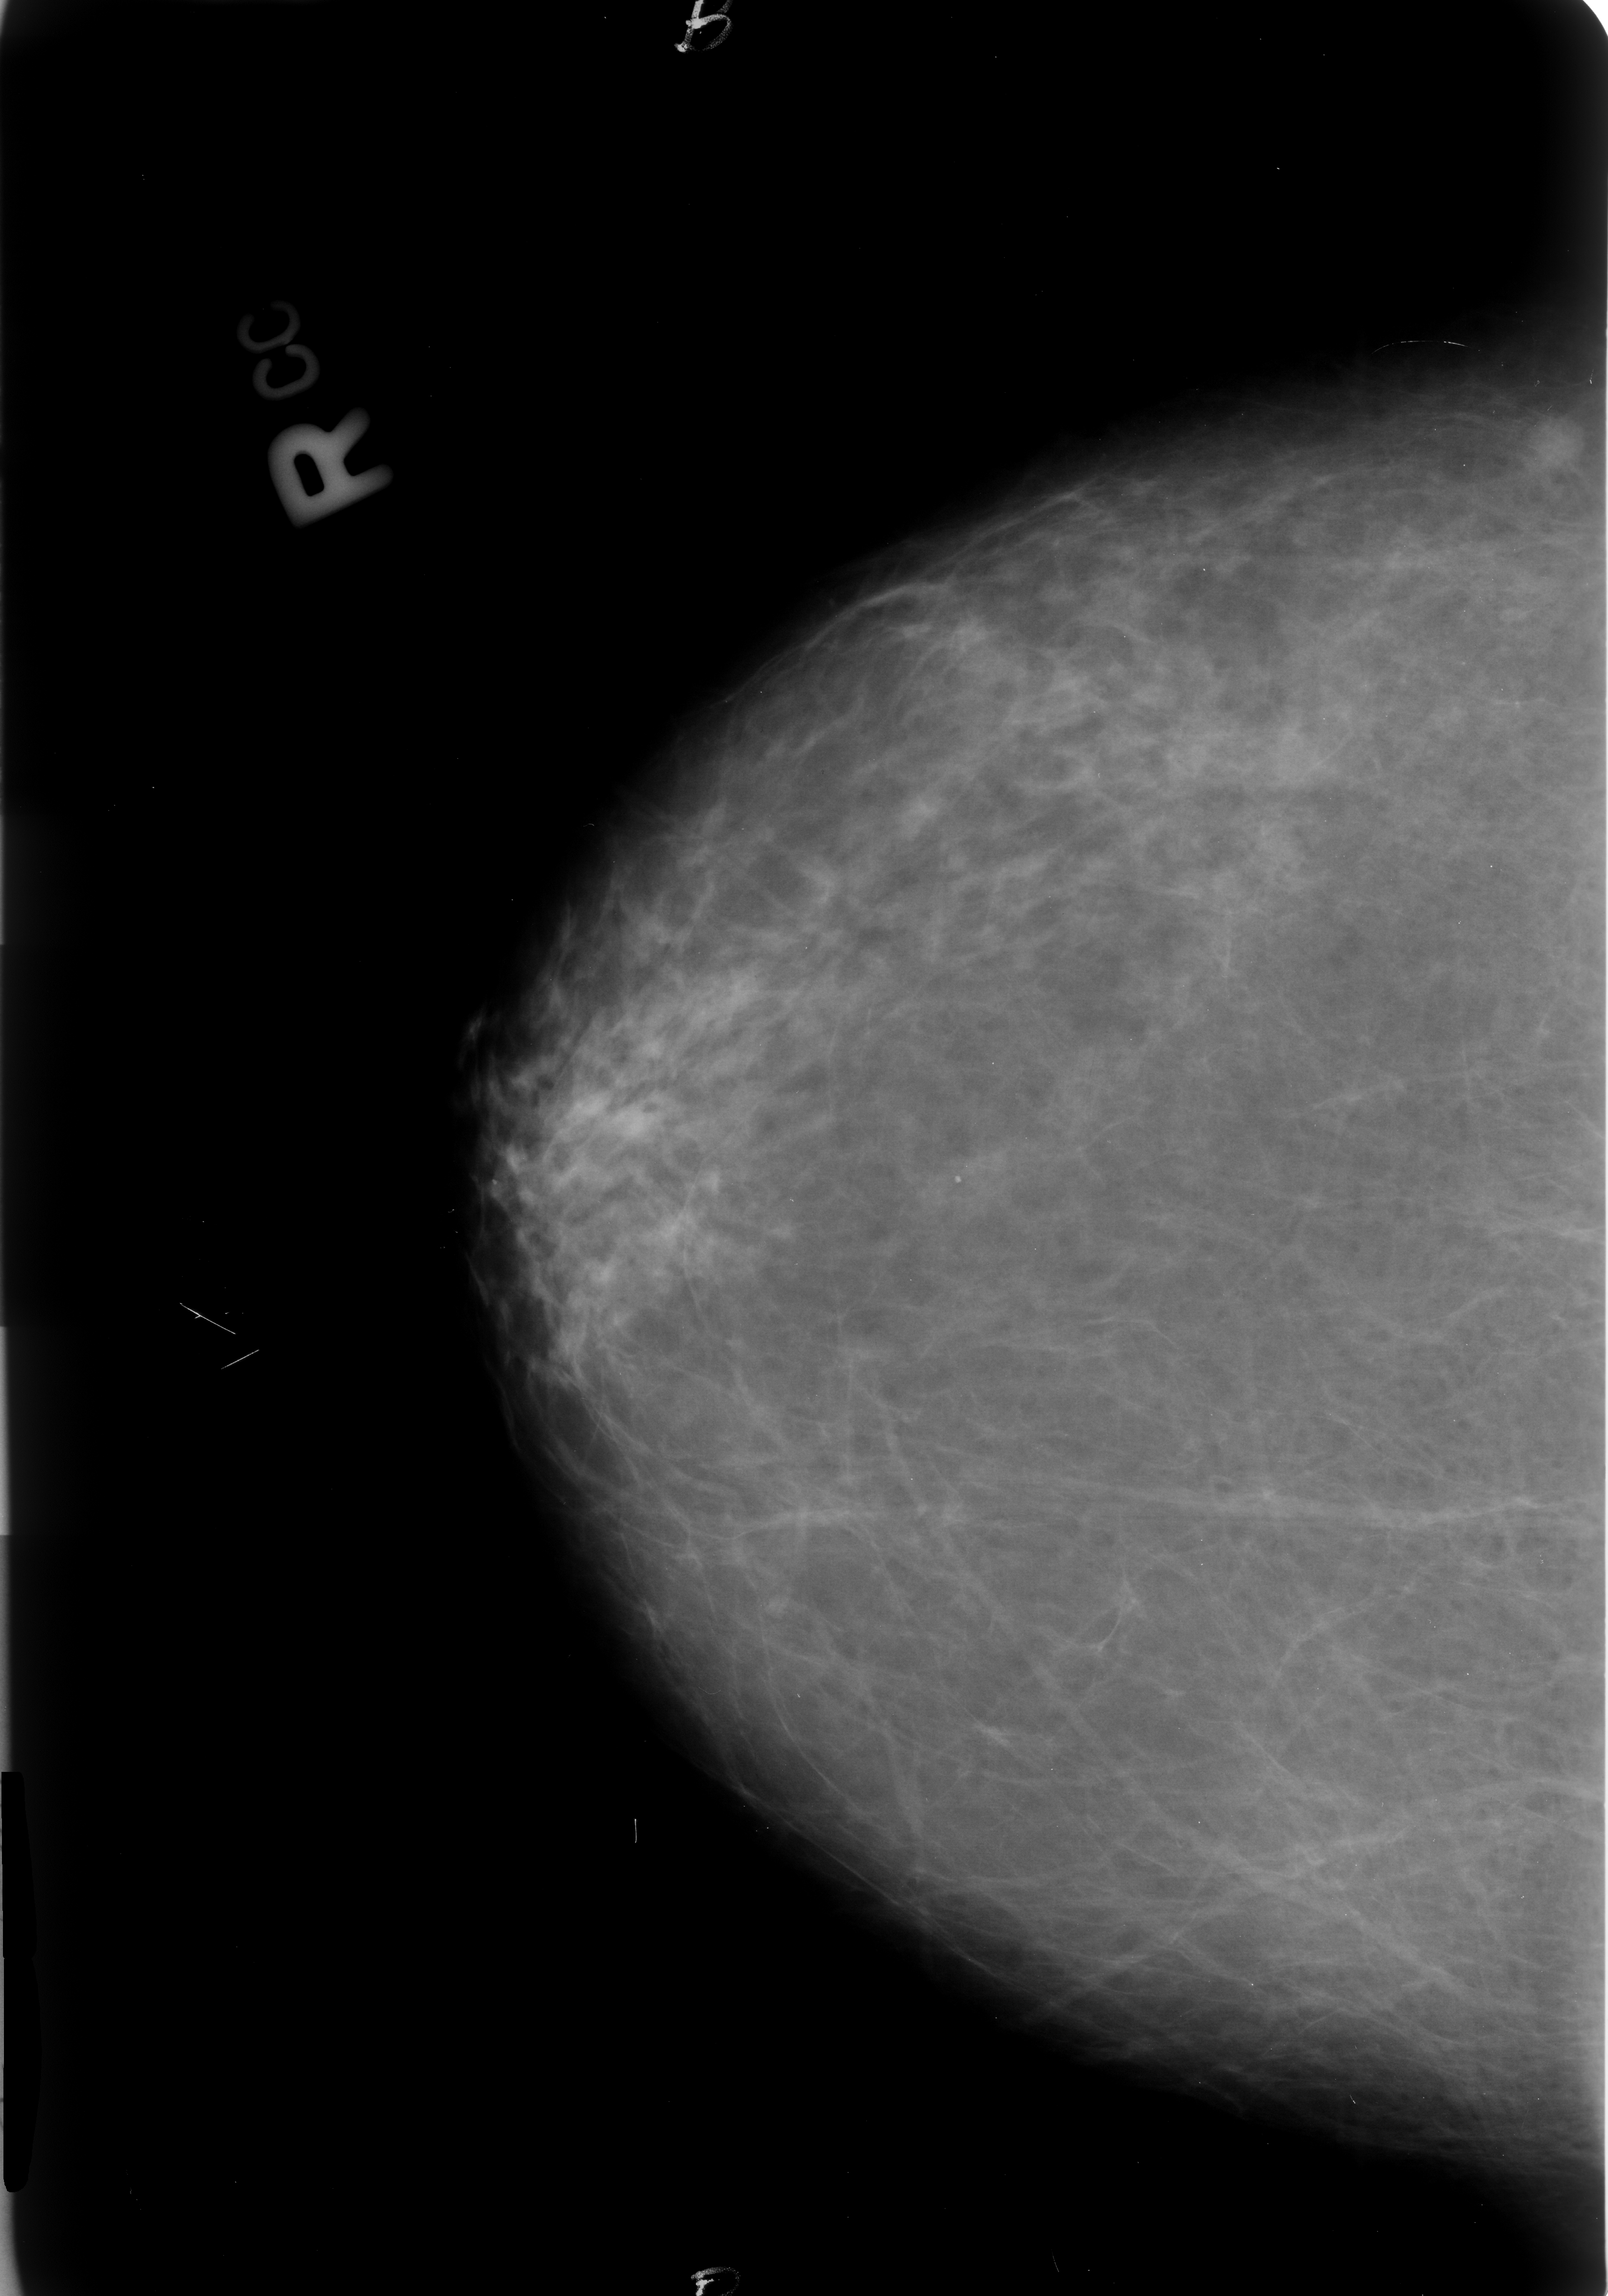
Scanned film-screen mammogram, right breast, craniocaudal (CC) view, breast composition: almost entirely fatty (BI-RADS density category 1 of 4).
Mass, shape oval, margins ill defined; BI-RADS assessment category 4; pathology result (as recorded, not read from the image): malignant.